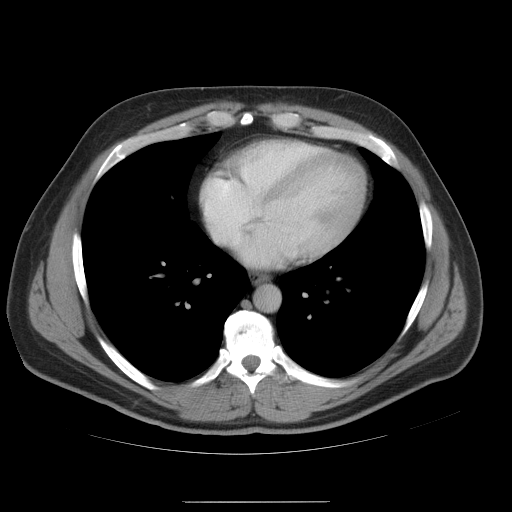
Contrast-enhanced abdominal CT, one axial slice. 120 kVp. Intravenous contrast given. Soft-tissue window (W 400 / L 40 HU). 5 mm slice thickness. 512 × 512 image matrix. Male patient, age 40 years. Case-level facts recorded for this patient, not image findings: diagnosis: colorectal cancer liver metastases, imaged before liver resection; multiple liver metastases: no; largest metastasis: 15 cm; disease in both lobes: no.
Structures marked on this image (manually delineated by an expert):
- hepatic veins: bounding box [x1, y1, x2, y2] px = [212, 201, 260, 236]